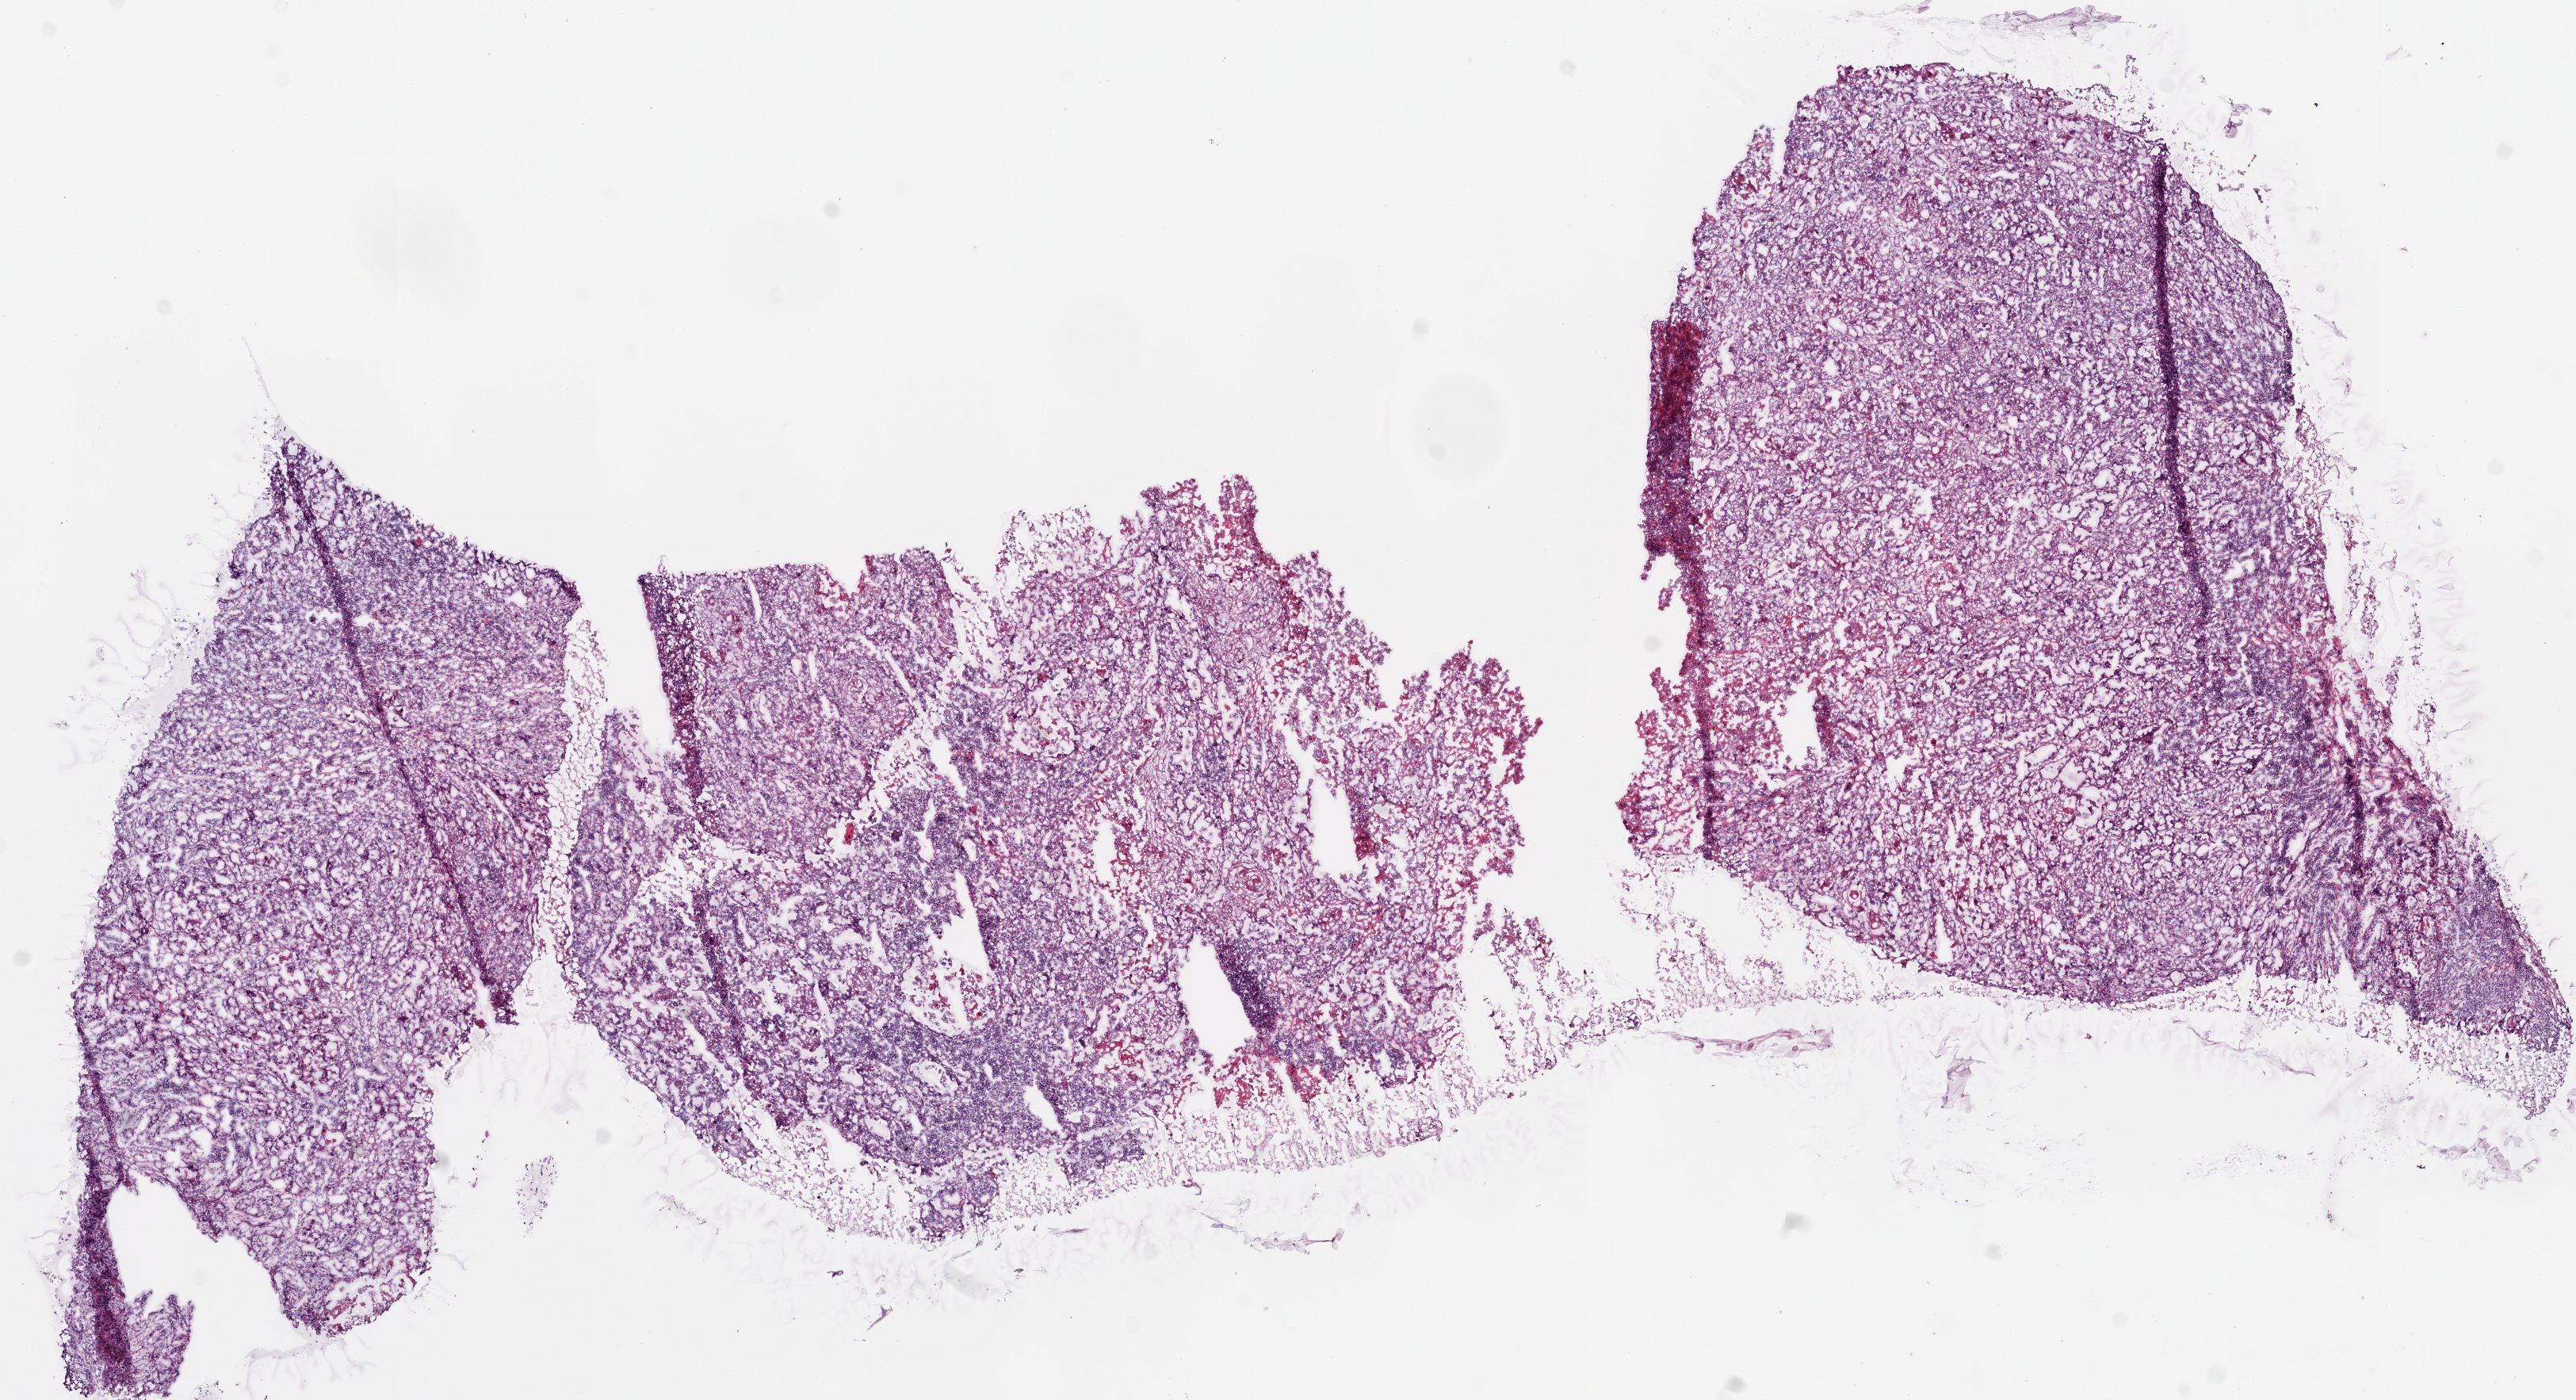
Digitized H&E tissue section (whole slide) — a low-resolution overview of the entire scanned area, about 13.0 x 7.1 mm. Frozen section from the bottom of the tissue portion. Sample: primary tumour, lung. Patient: female, age at initial diagnosis 62 years. Pathologist review of this section (percent, as recorded): tumour cells 80%, tumour nuclei 65%, normal cells 0%, stromal cells 10%, necrosis 10%.
Diagnosis: Squamous cell carcinoma, NOS. AJCC pathologic stage: IIB. Laterality: right. TNM: T2 N1 M0.